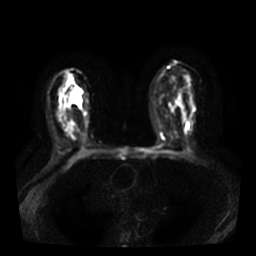
Breast MRI, one axial slice. Diffusion-weighted series; image 2 of 4 stored at this slice position (different b-values; order by instance number). 3 T. 5 mm slice thickness. 256 × 256 image matrix. Female patient.
Structures marked on this image (expert manual segmentation):
- tumour on diffusion-weighted imaging: bounding box (x1, y1, x2, y2) in pixels: (71, 89, 81, 104)